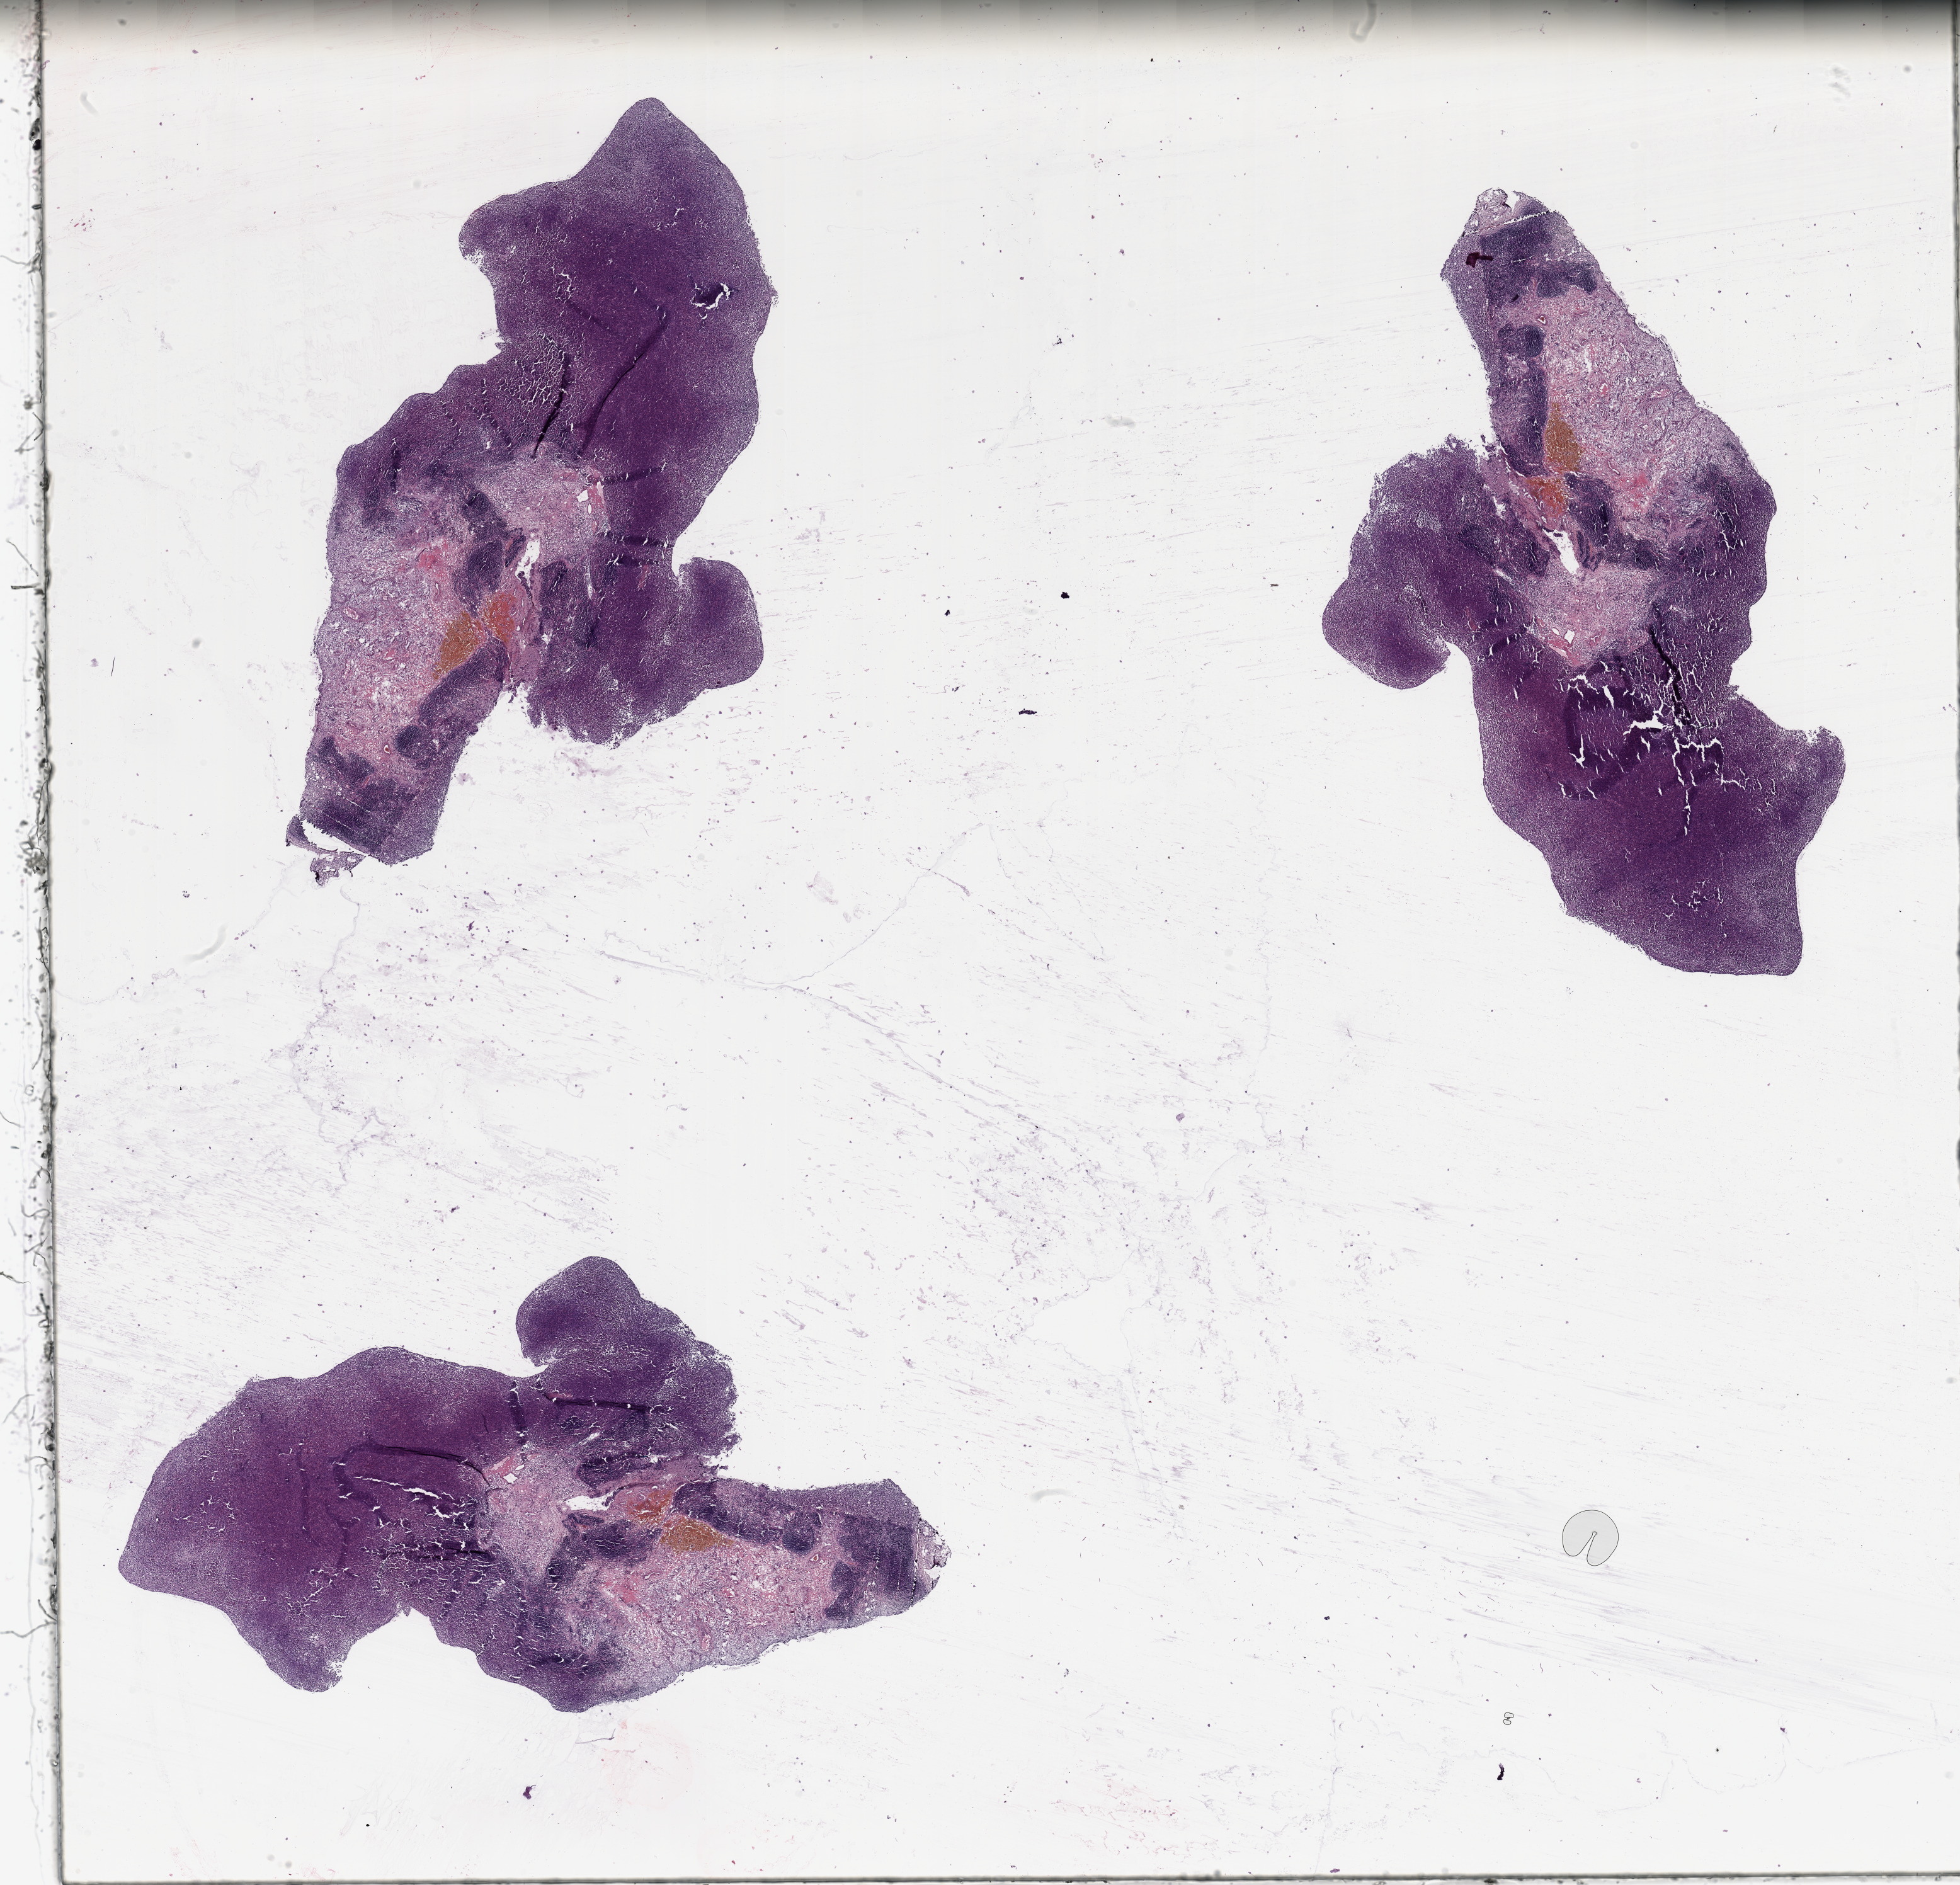
H&E whole-slide image, a low-resolution overview of the entire scanned area, about 24.6 x 23.7 mm (from a 20x scan); melanoma tumour tissue; sampled site not recorded. 46-year-old female patient.
* diagnosis: Malignant melanoma, NOS
* primary tumour site (as recorded): extremities
* AJCC pathologic stage: IIC